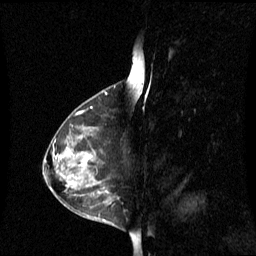
Breast MRI (dynamic contrast-enhanced), one sagittal slice. Dynamic contrast-enhanced series, image 2 of 3 at this slice position (ordered by acquisition). 1.5 T. TE 4.2 ms, TR 8.4 ms. 2.1 mm slice thickness. 256 × 256 image matrix, field of view 240 × 240 mm. Female patient, age 42 years. Case-level facts recorded for this patient, not image findings: setting: breast cancer imaged before/during neoadjuvant chemotherapy; receptor status: HR-positive, HER2-negative.
Outlined on this slice (semi-automatically segmented with operator editing):
- analysis volume of interest (the breast-tissue region the enhancement analysis was run in; not a lesion): bounding box <60,128,108,195> (left, top, right, bottom; pixels)
- tumour enhancement mask (voxels above the 70 % enhancement threshold inside the analysis volume of interest): <82,156,91,165>